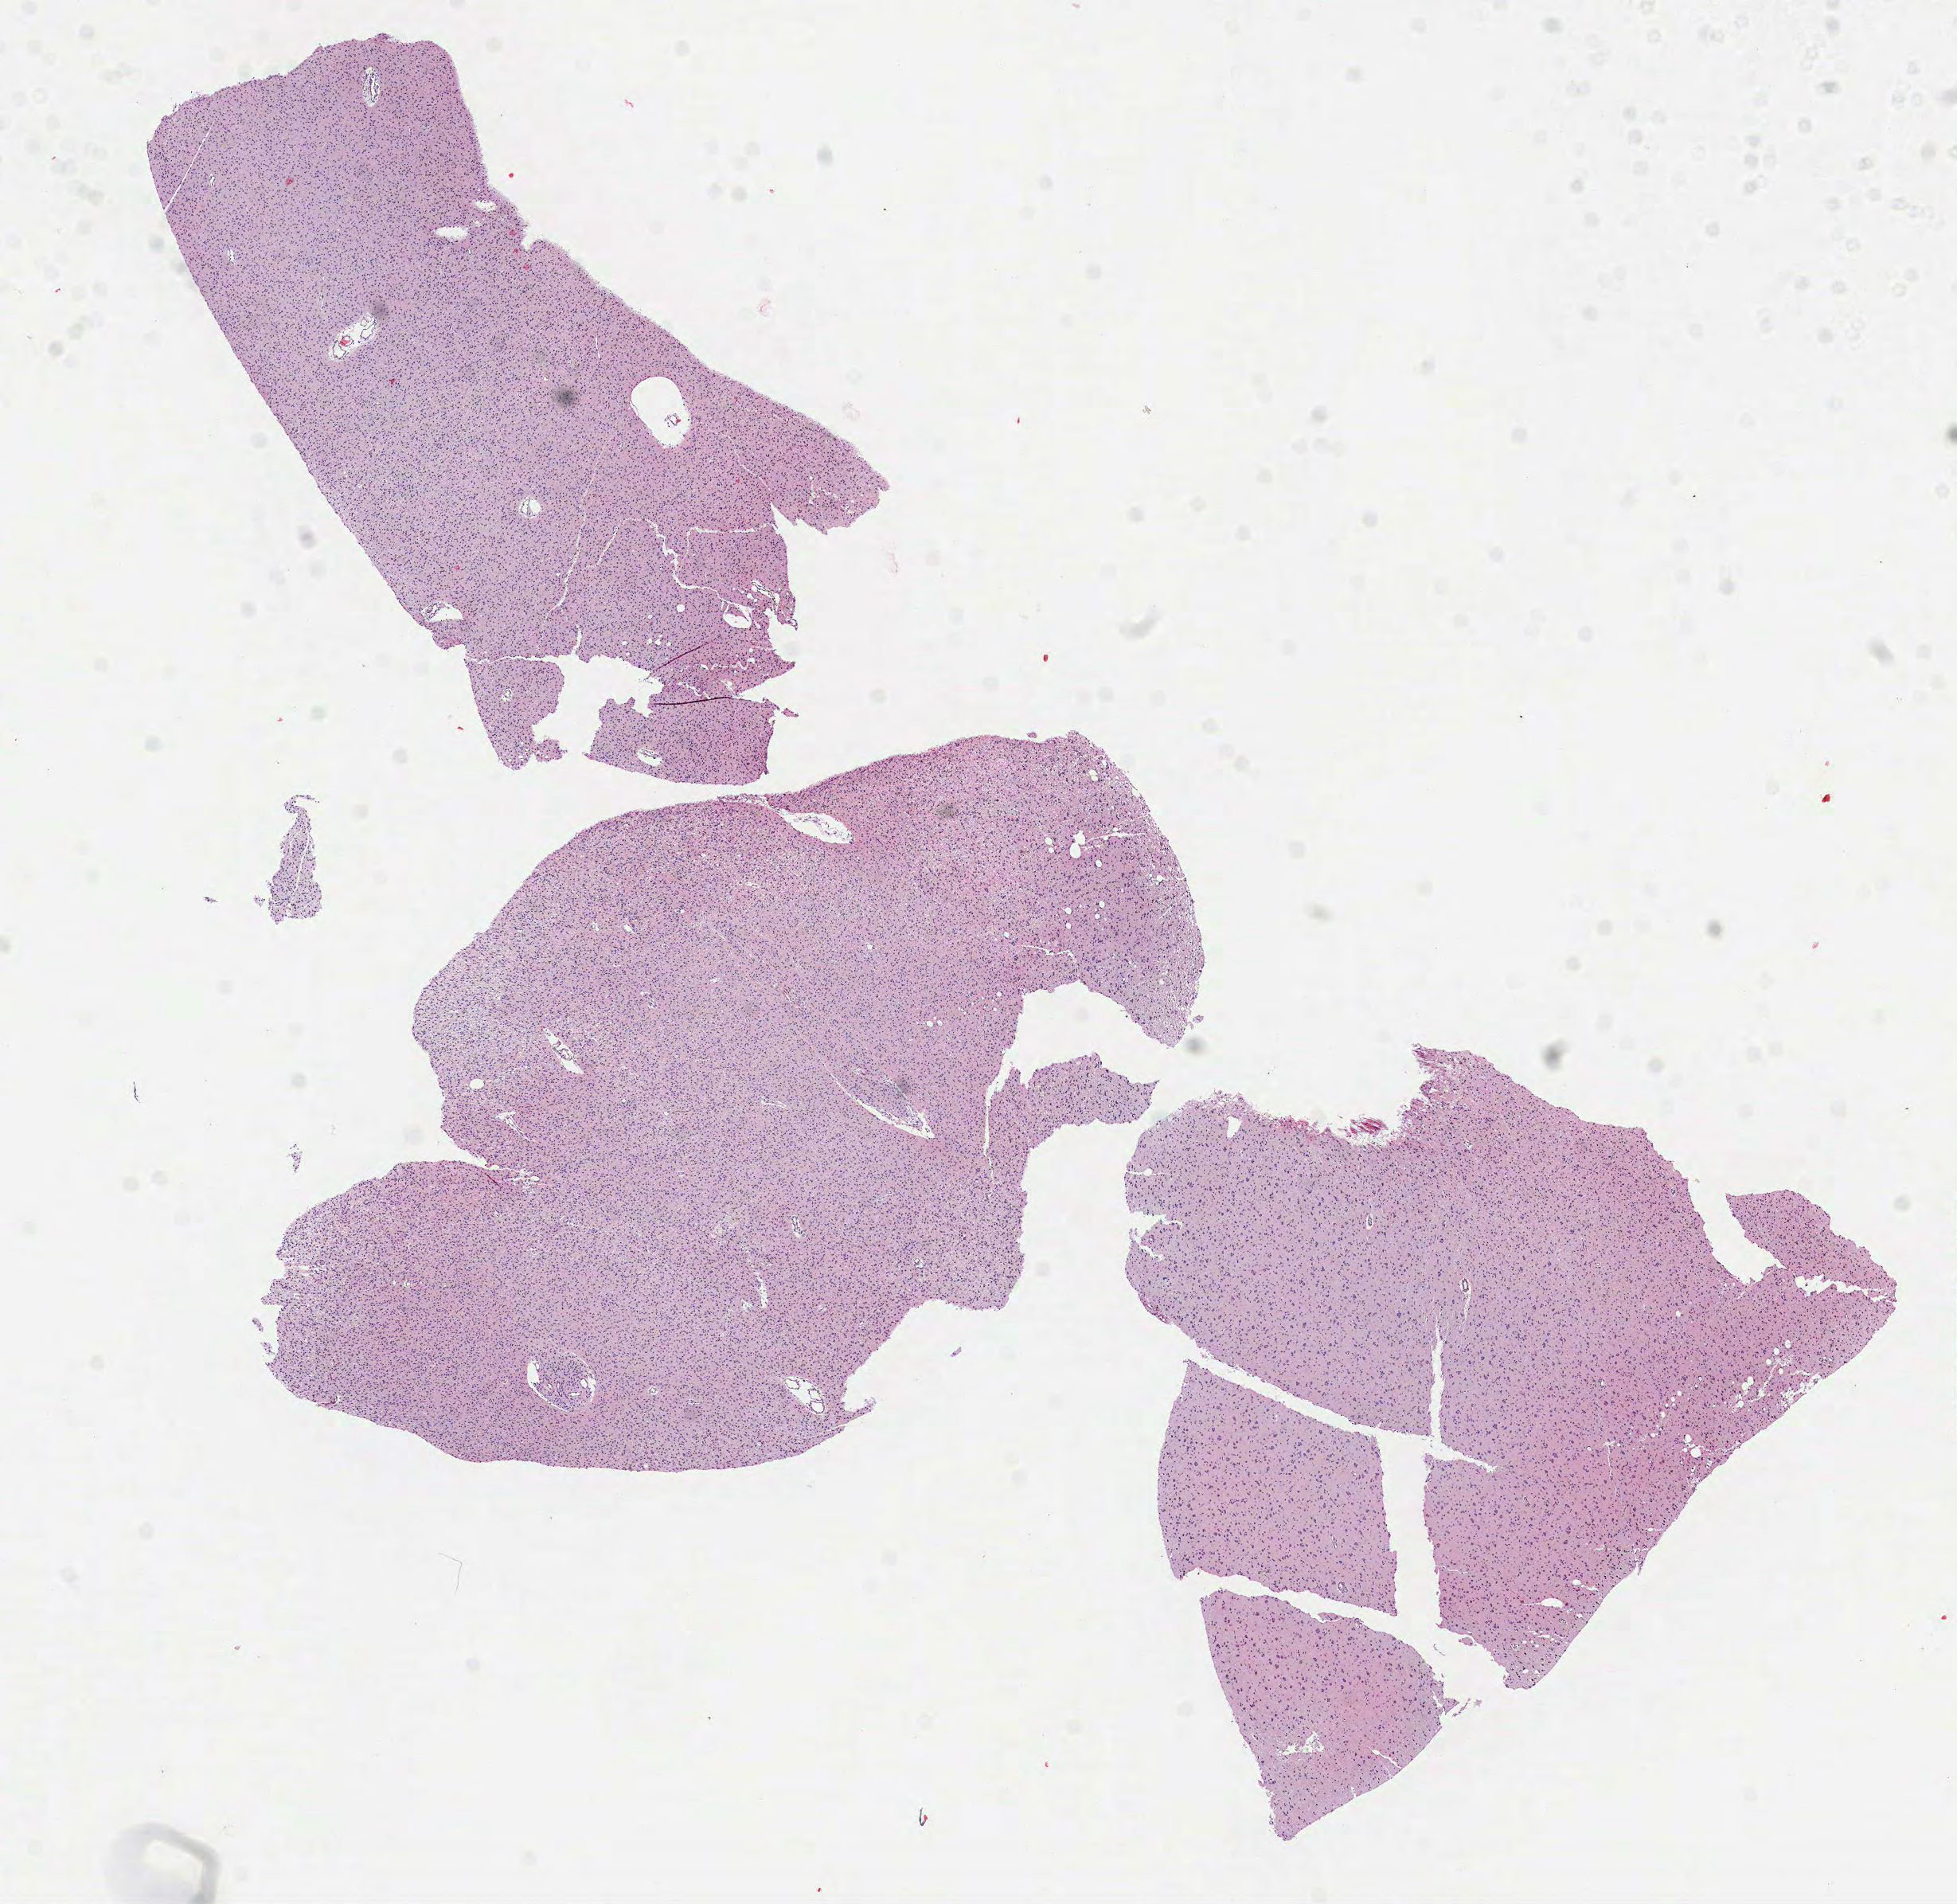
Hematoxylin and eosin (H&E) stained whole-slide image — low-resolution overview of the scanned area, about 9.9 x 9.6 mm (slide scanned at 40x); formalin-fixed paraffin-embedded (FFPE) diagnostic section; sample: primary tumour, brain. Female patient; age at initial diagnosis 34 years. Histologic grade: G2 (moderately differentiated).
Diagnosis: Oligodendroglioma, NOS.